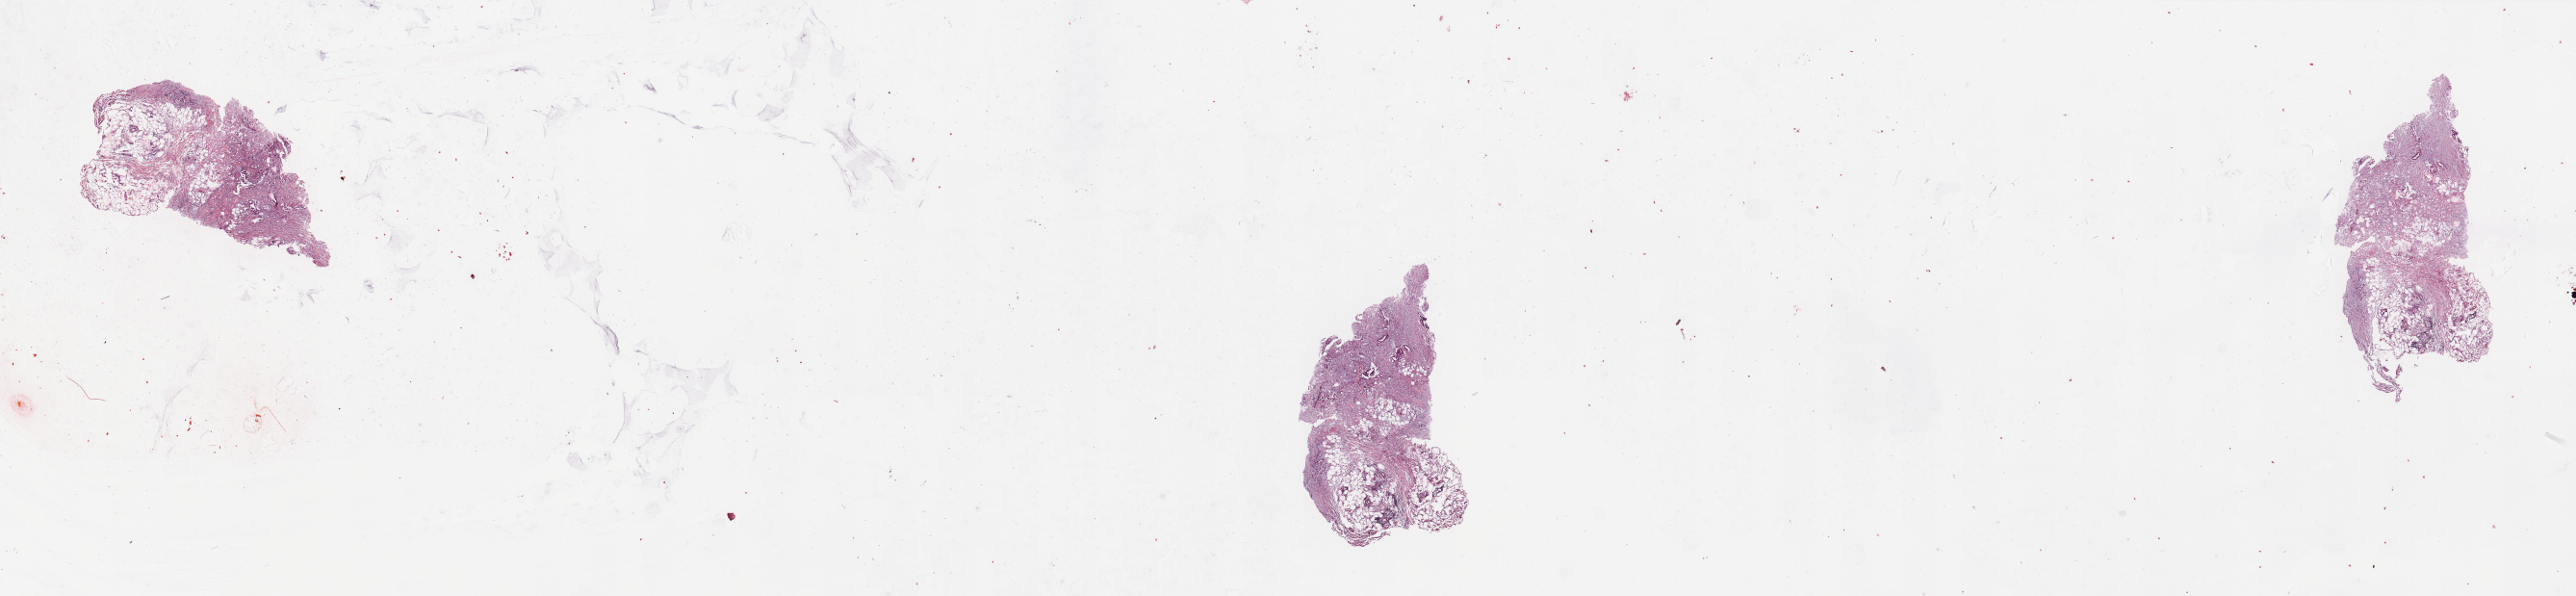
Digitized H&E-stained tissue section (whole slide), a low-resolution overview of the entire scanned area, about 42.3 x 9.8 mm (acquisition: 20x scan). Tumour tissue sample, pancreas. Patient: male, age 42 years.
Patient diagnosis (cohort enrolment): ductal adenocarcinoma (pancreas). Primary tumour site (as recorded): head.